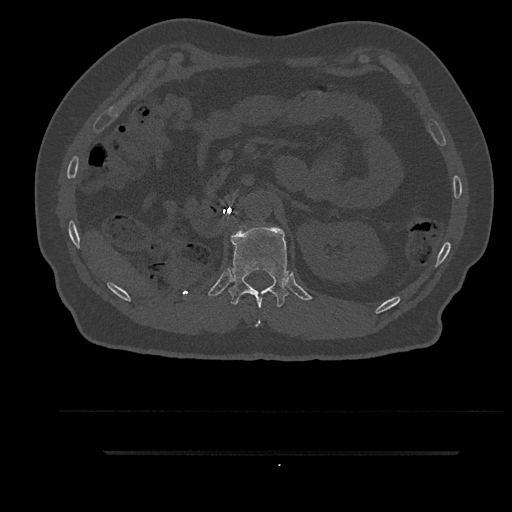
CT including the spine, one axial slice; slice 239 of 797 in the series (ordered by position); bone window (W 1800 / L 400 HU); 0.5 mm slice thickness; 512 × 512 image matrix, field of view 432 × 432 mm. Male patient, age 63 years. From the clinical record (not read from this slice): primary cancer: renal; vertebrae with lytic lesions (as recorded): T8.
Annotated regions visible in this slice (semi-automatic segmentation, software-assisted and operator-edited):
- T12 vertebra: box from (x=228, y=225) to (x=289, y=326) px